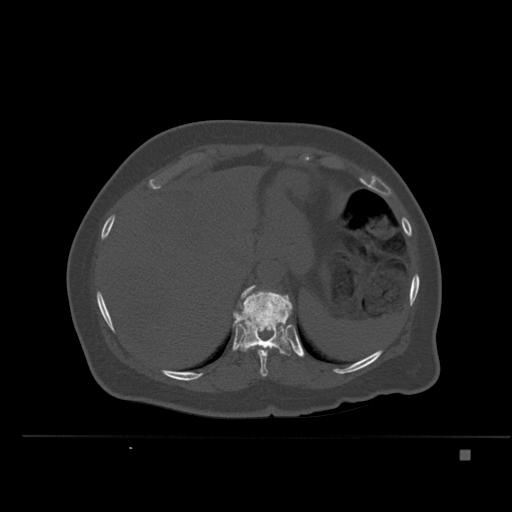
CT including the spine, one axial slice; slice 272 of 477 in the series (ordered by position); bone window (W 1800 / L 400 HU); 512 × 512 image matrix. Female patient, age 74 years. From the clinical record (not read from this slice): primary cancer: colon.
Structures marked on this image (semi-automatically segmented with operator editing):
- T10 vertebra: bounding box (x1, y1, x2, y2) in pixels: (252, 345, 276, 377)
- T11 vertebra: (233, 286, 293, 355)